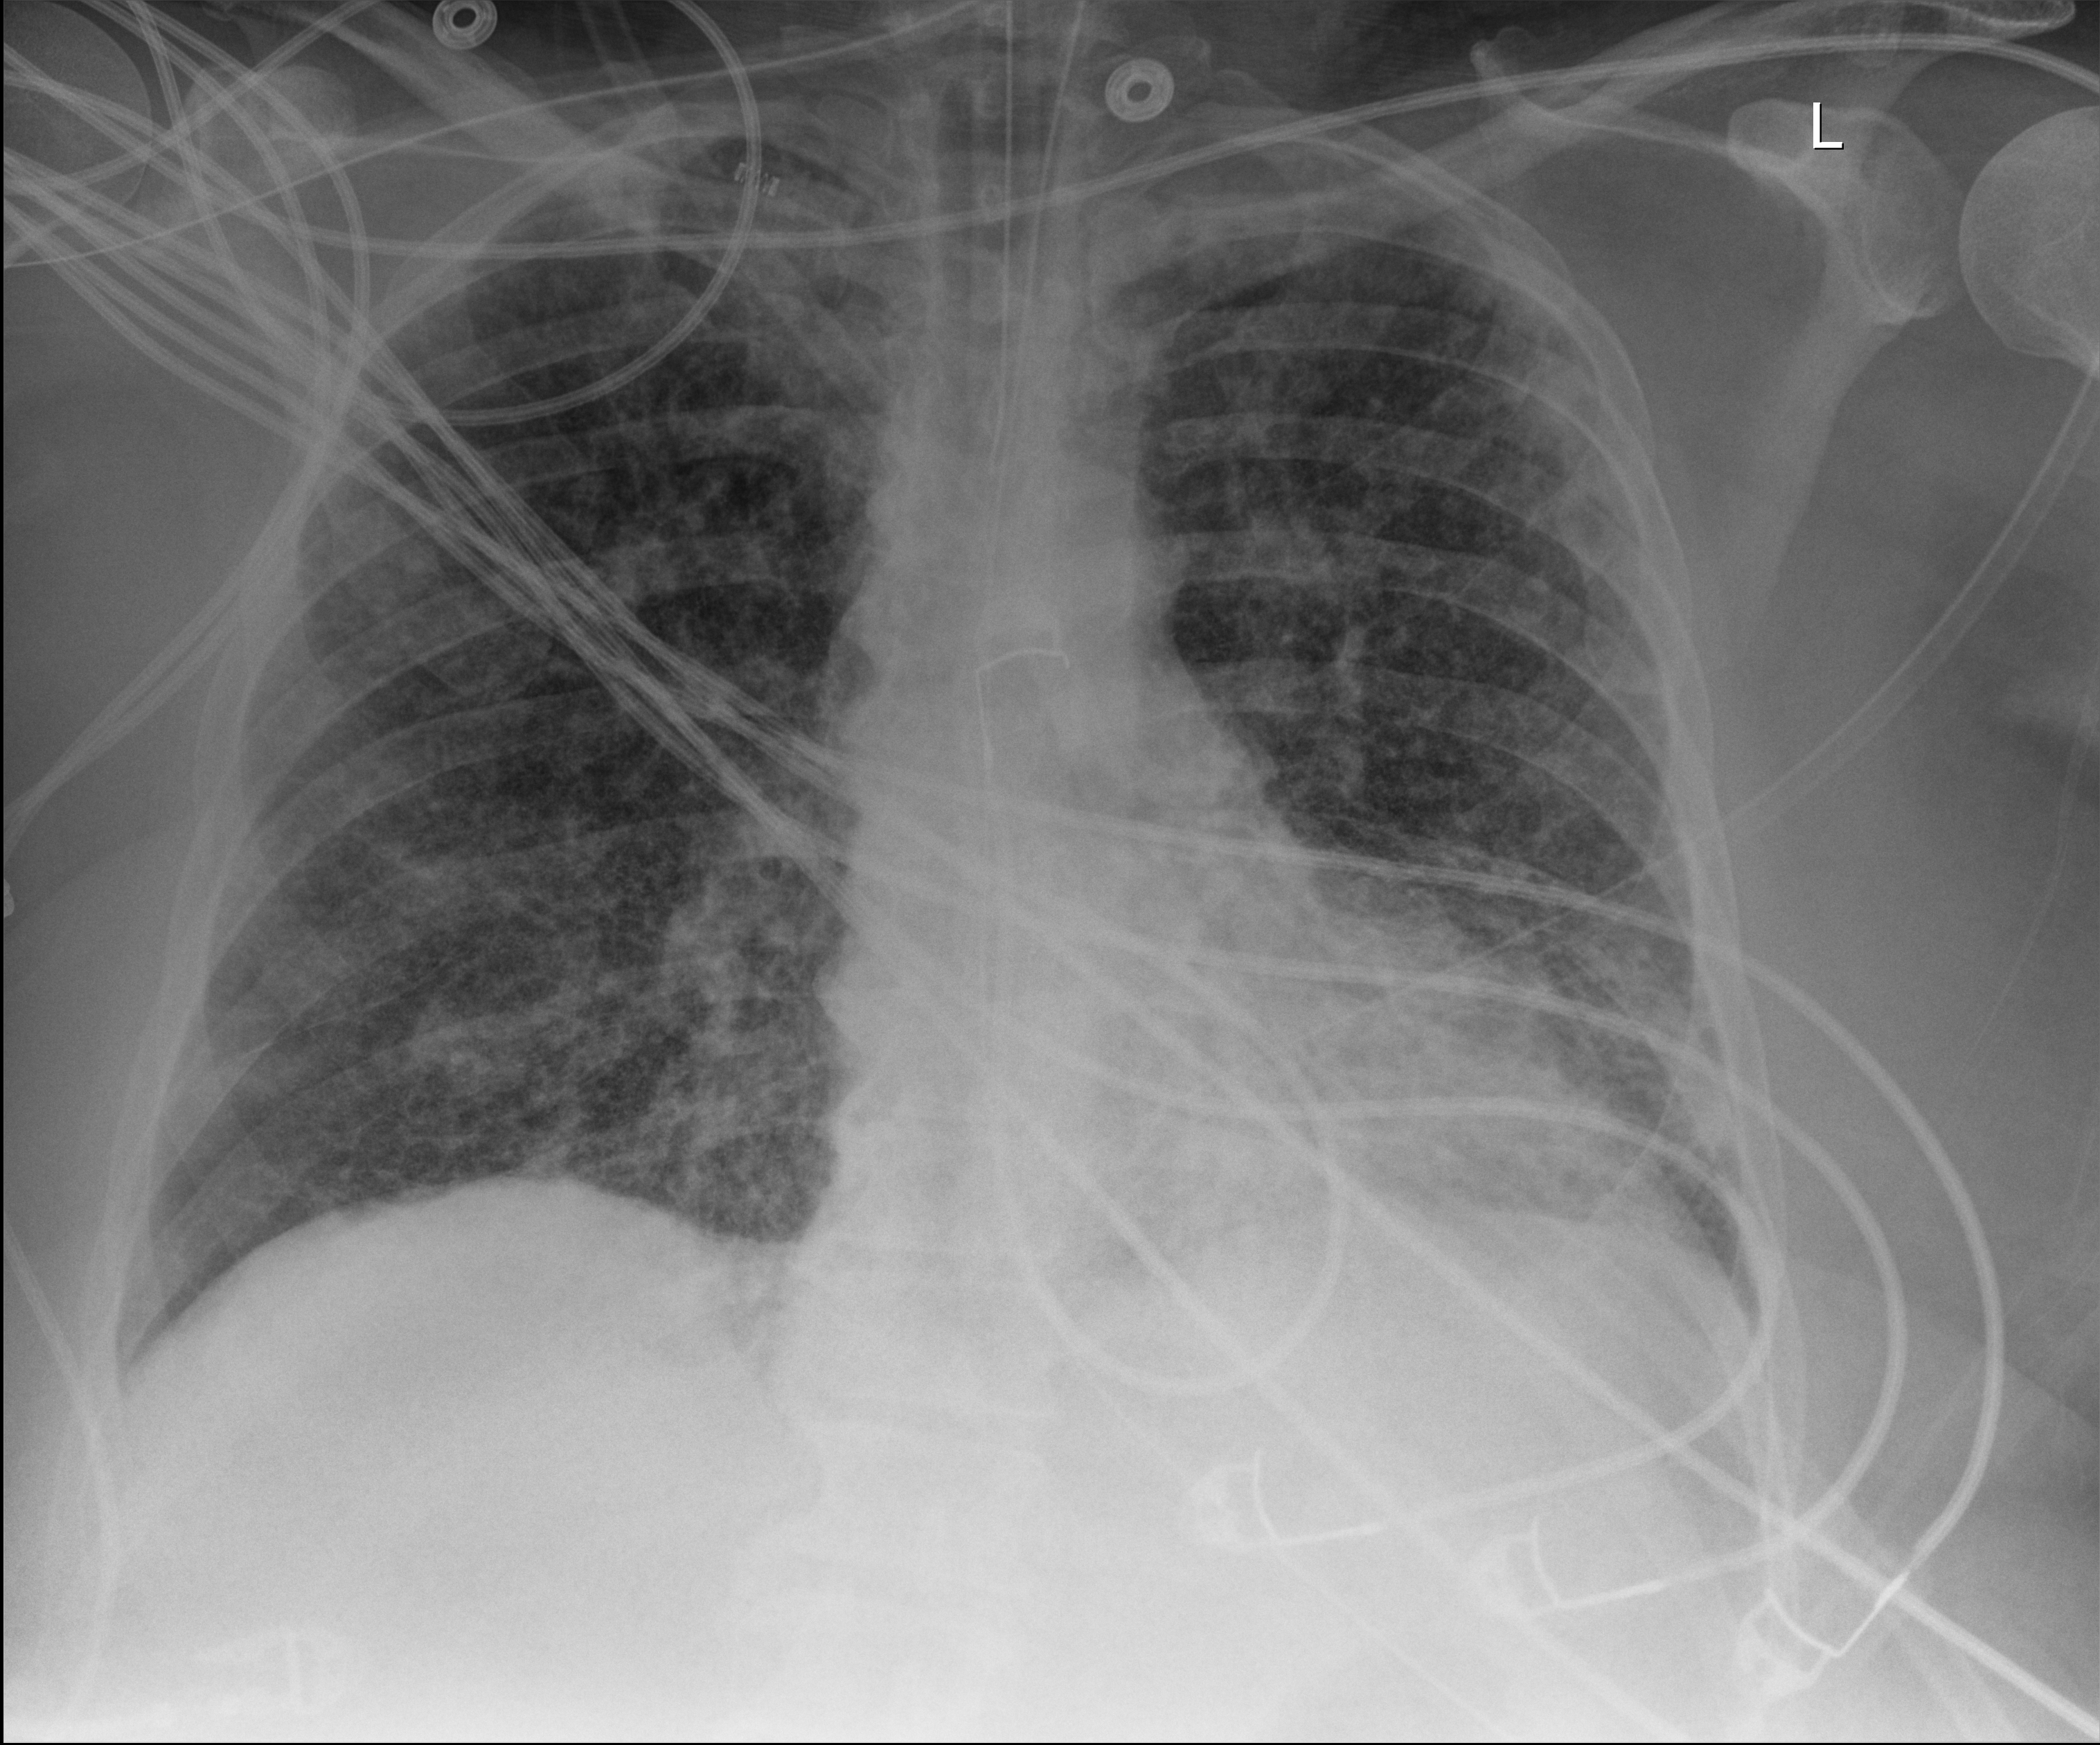
Chest X-ray; anteroposterior (AP) projection. Adult patient hospitalised with COVID-19, age 18–59 years.
Hospital-stay facts (about this admission, not read from this image; timing relative to this image not recorded):
- mechanically ventilated during this hospital stay: yes
- admitted to intensive care during this hospital stay: yes